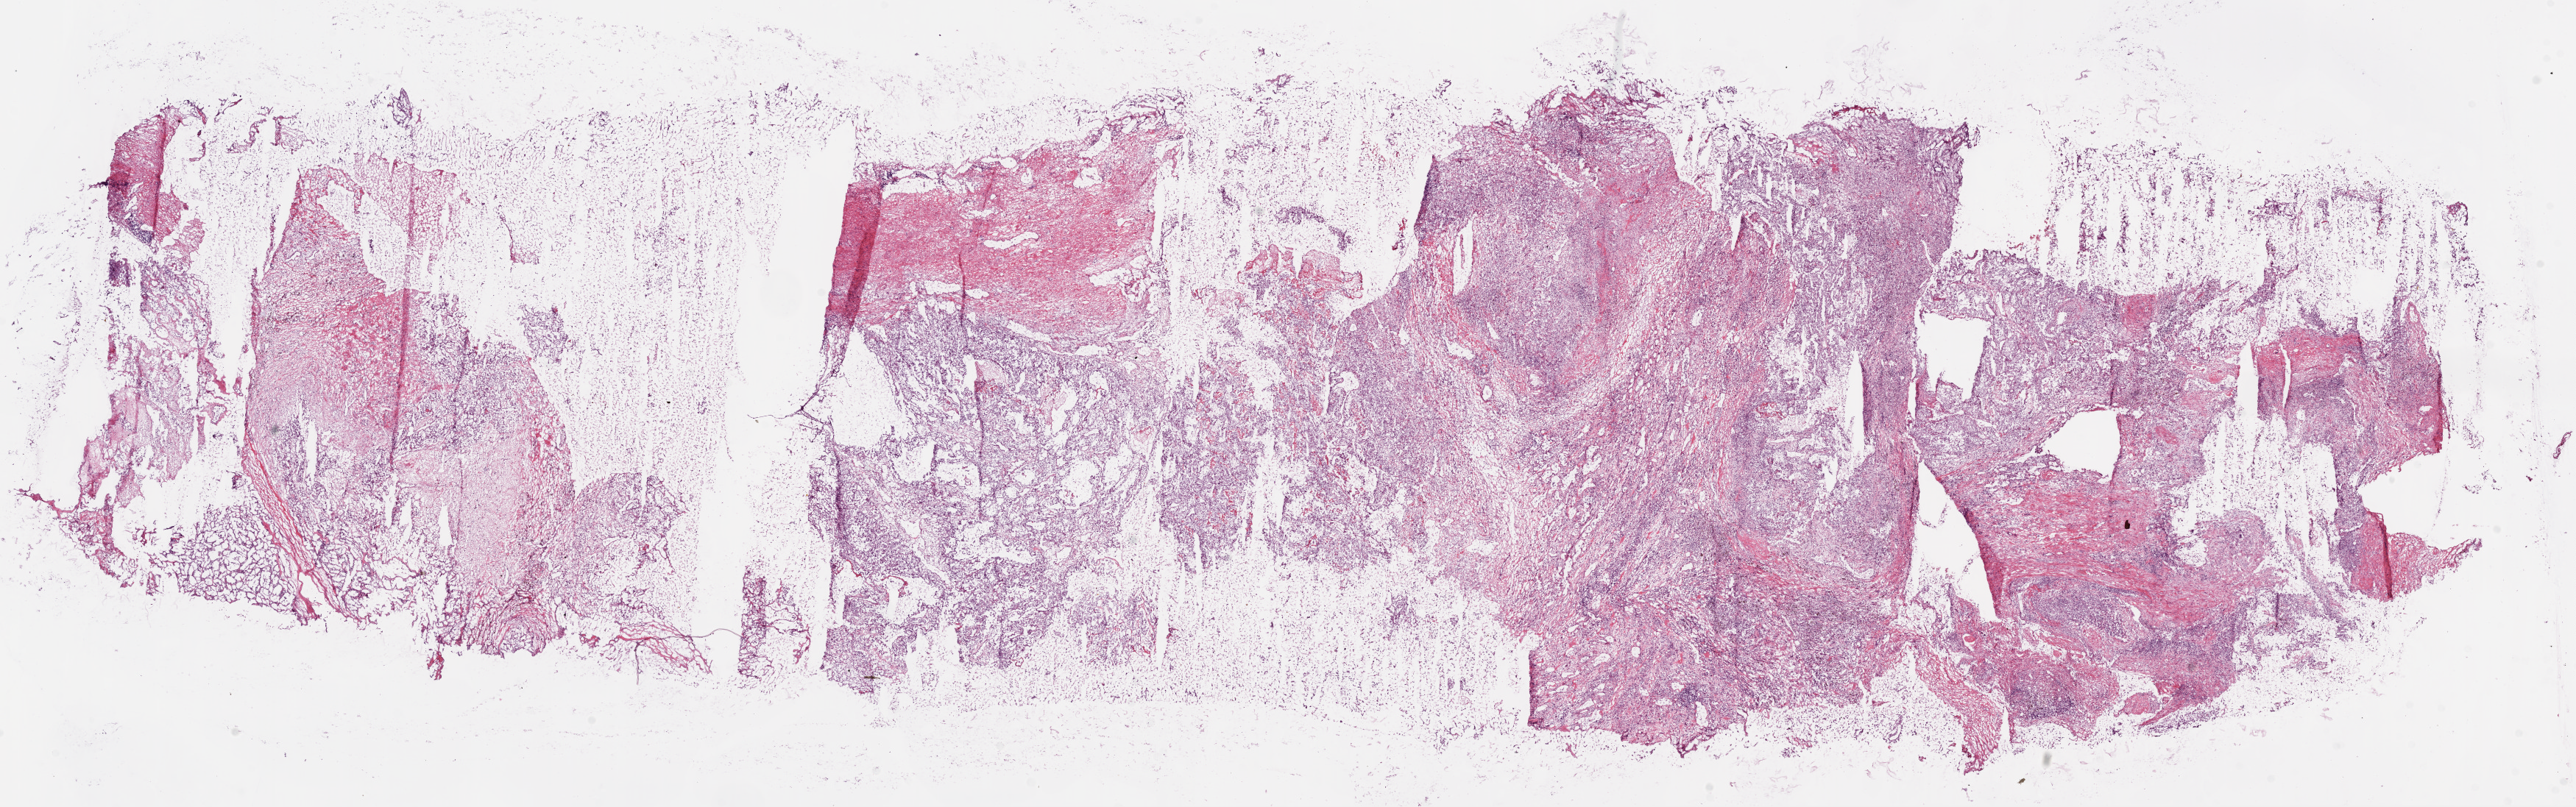
H&E-stained whole-slide image — a low-resolution overview of the entire scanned area, about 28.1 x 8.8 mm (slide scanned at 20x), frozen section from the bottom of the tissue portion, primary tumour sample from the kidney. Patient: male, age at initial diagnosis 72 years. Histologic grade: G4 (undifferentiated). Slide review estimates, as recorded: tumour cells 80%, tumour nuclei 75%, normal cells 0%, stromal cells 20%, necrosis 0%.
Lymph nodes positive (case pathology): 0 of 1 examined. Histologic diagnosis: Clear cell adenocarcinoma, NOS. AJCC pathologic stage: IV (7th edition).